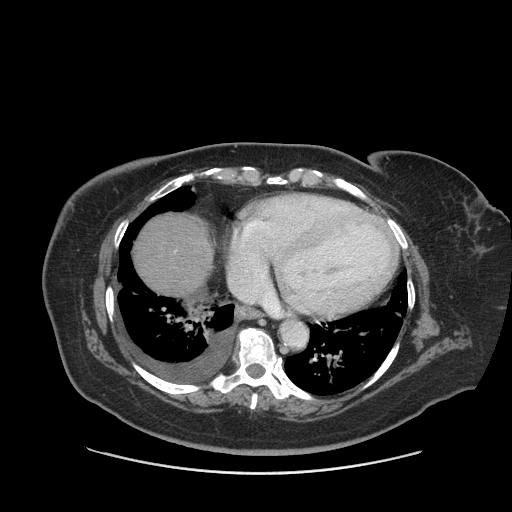
Contrast-enhanced abdominal CT (liver protocol), one axial slice; position 82 of 91 along the scan axis; reconstruction kernel STANDARD; 140 kVp; soft-tissue window (W 400 / L 40 HU); 512 × 512 image matrix. Case-level facts recorded for this patient, not image findings: diagnosis: hepatocellular carcinoma (patient treated with transarterial chemoembolisation; whether this scan precedes or follows treatment is not stated here); TNM stage (as recorded): Stage-I; Child-Pugh class: A.
Outlined on this slice (semi-automatic segmentation, software-assisted and operator-edited):
- abdominal aorta: box from (x=281, y=320) to (x=307, y=346) px
- liver parenchyma outside the tumour (the mass and vessels are separate outlines, so this box may not span the whole liver): (x=132, y=212)–(x=212, y=292)